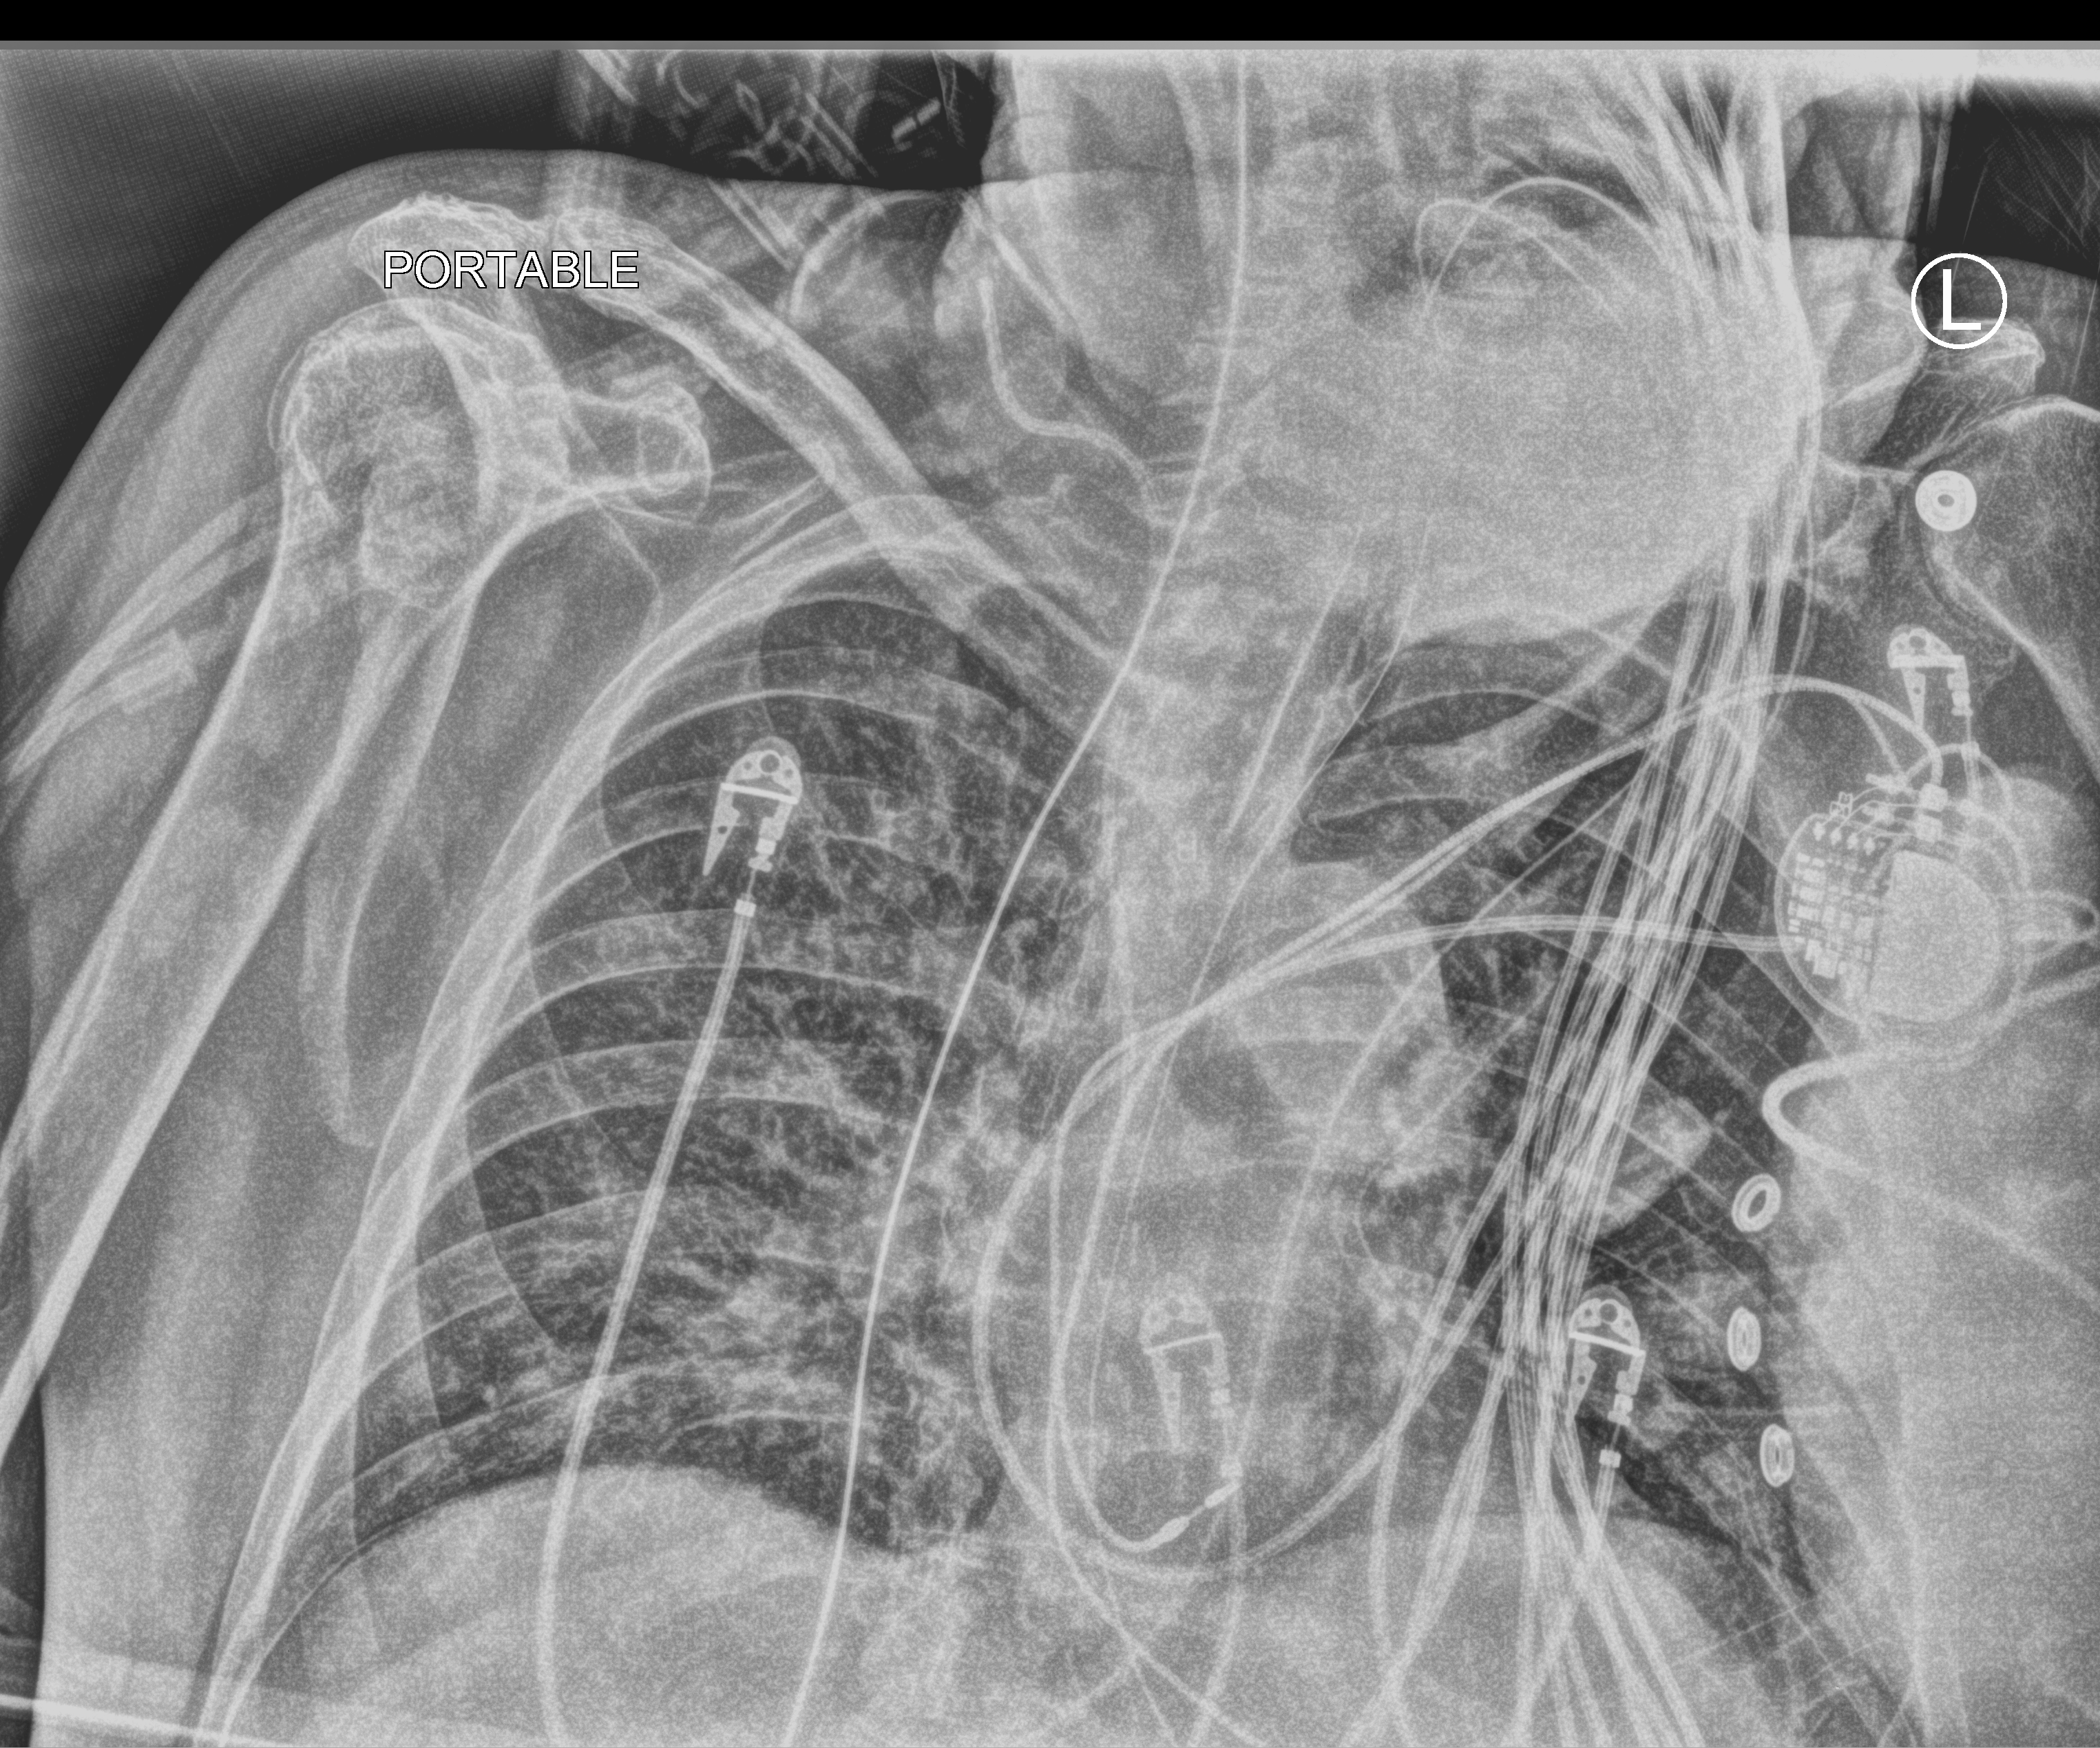
Chest X-ray (portable), anteroposterior (AP) projection. Patient hospitalised with COVID-19; male, aged 60–74 years.
Hospital-stay facts (about this admission, not read from this image; timing relative to this image not recorded):
- admitted to intensive care during this hospital stay: no
- mechanically ventilated during this hospital stay: no